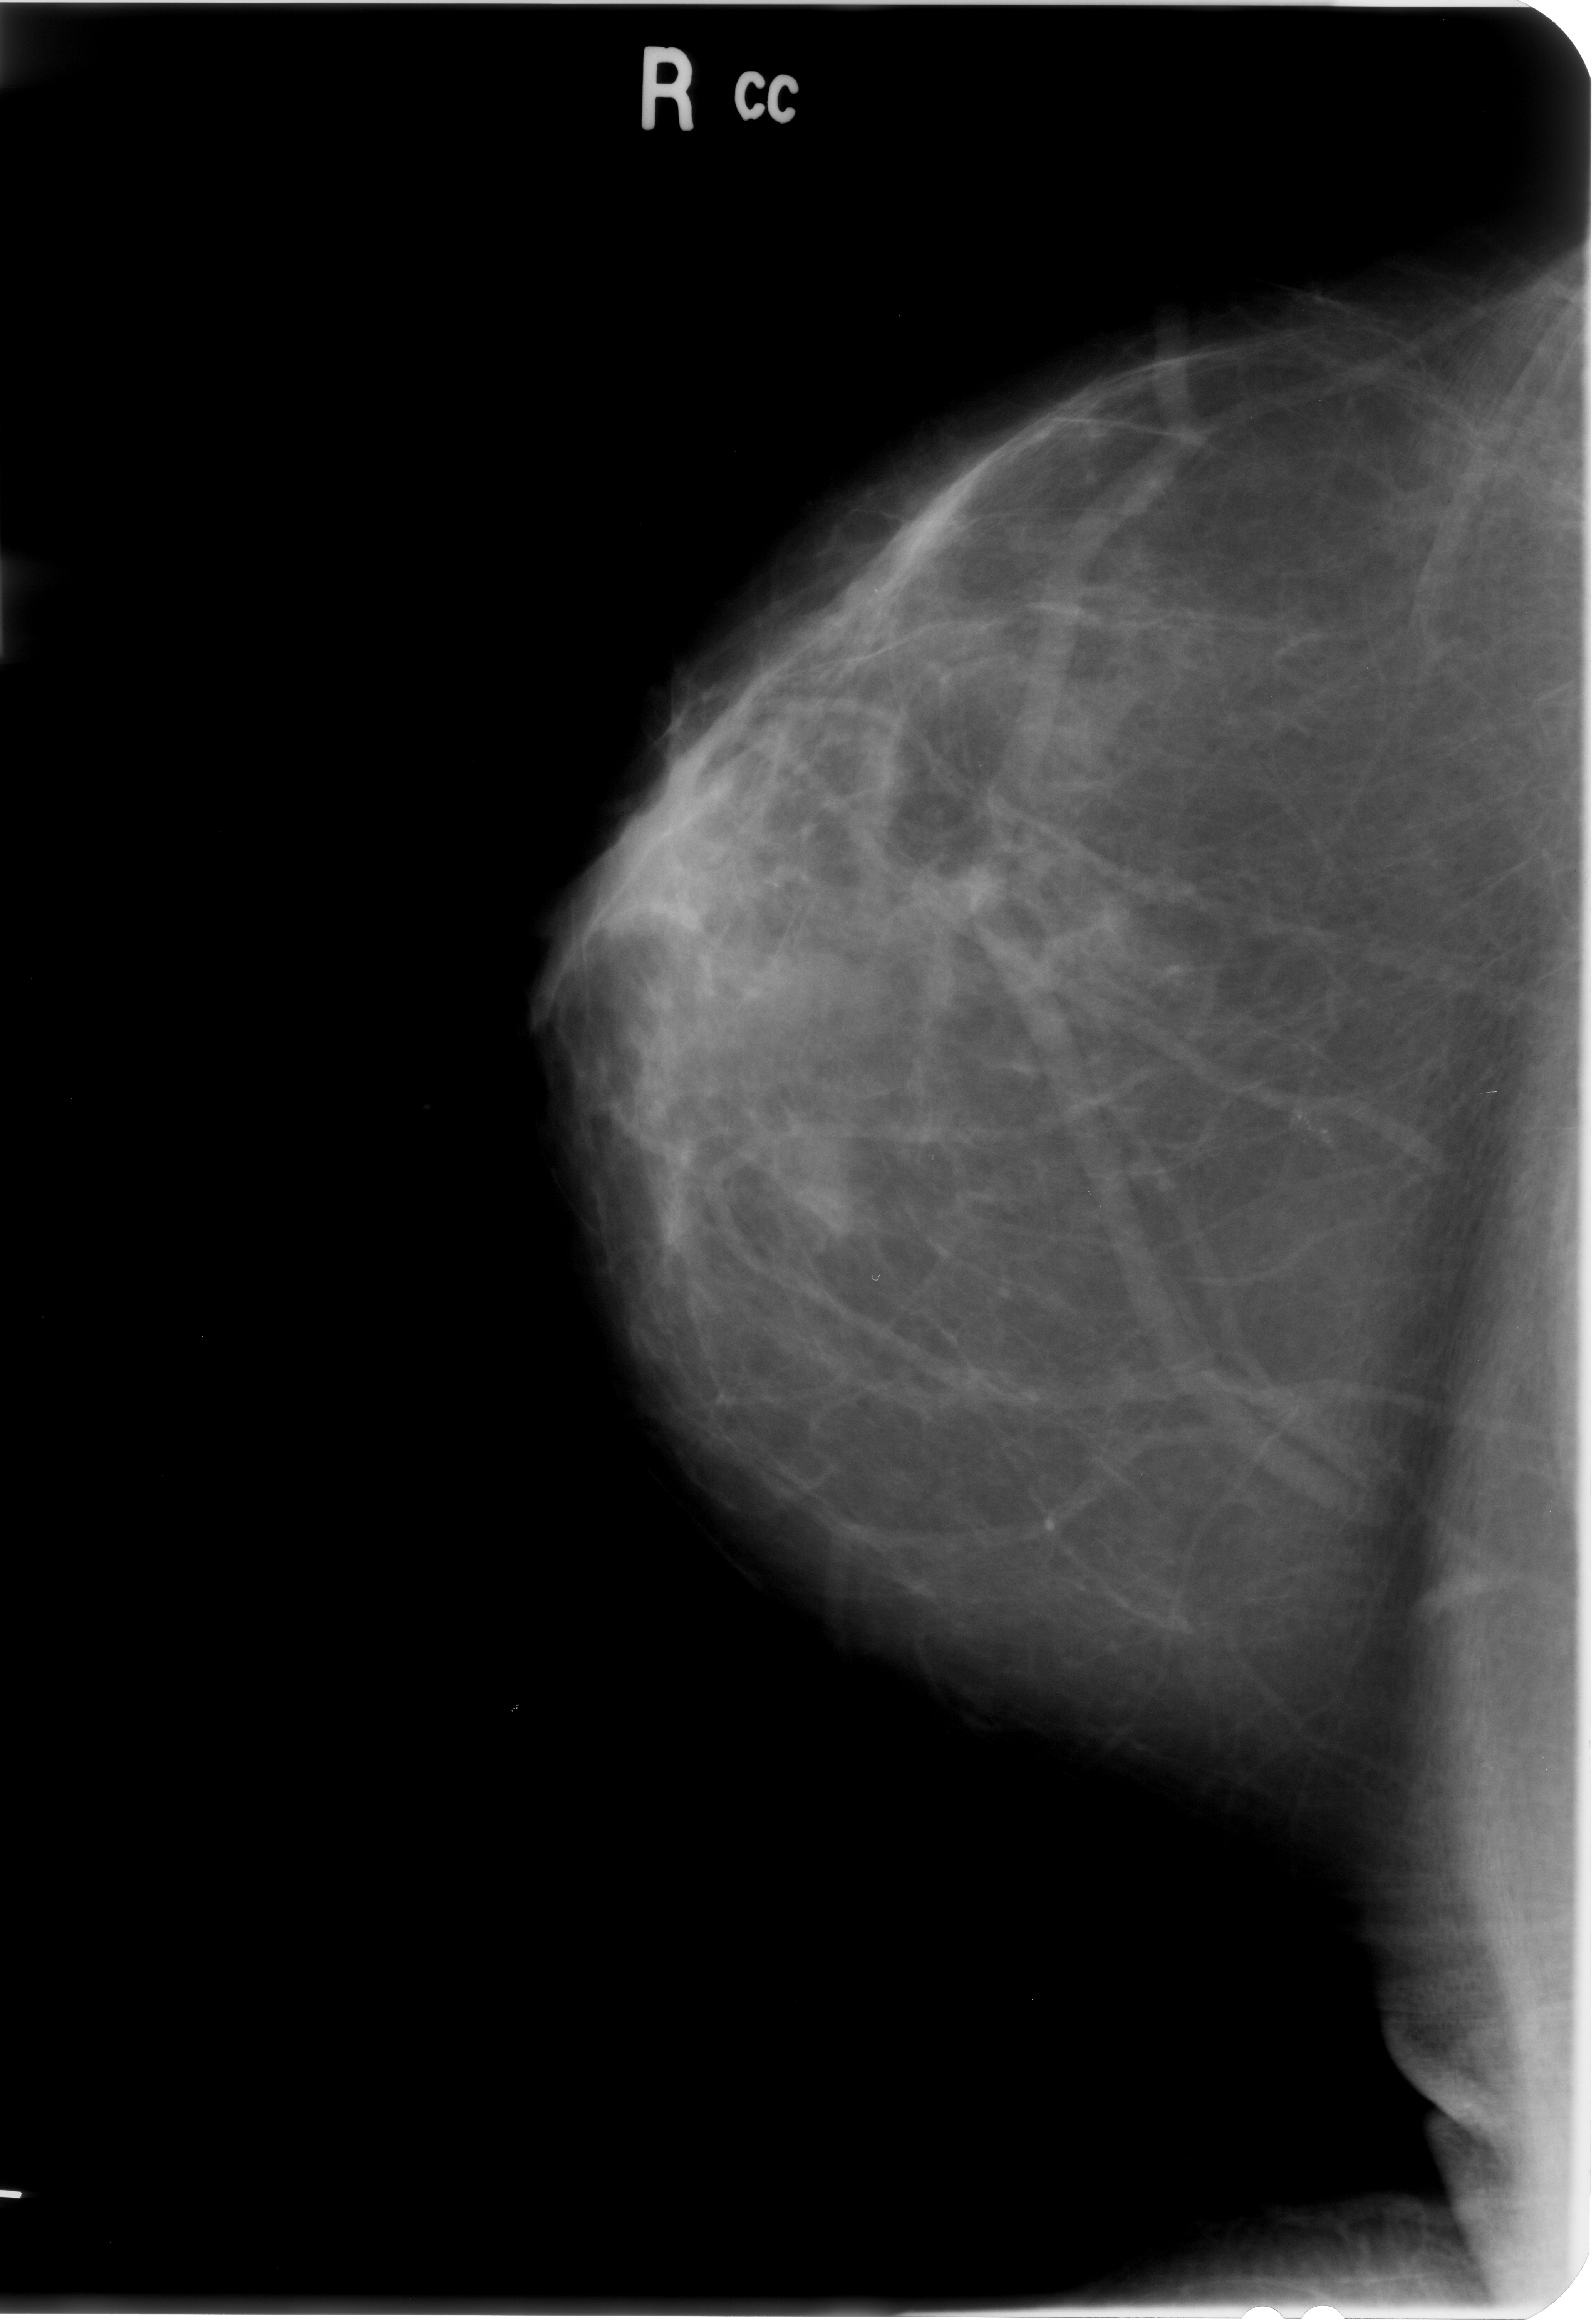
Mammogram (digitized film). Right breast. CC view. 1596 × 2320 image matrix.
Marked abnormalities (boxes around the expert regions of interest):
- calcifications, morphology pleomorphic, distribution clustered; BI-RADS assessment category 4; pathology (as recorded): benign: bounding box <1278,1096,1360,1178> (left, top, right, bottom; pixels)